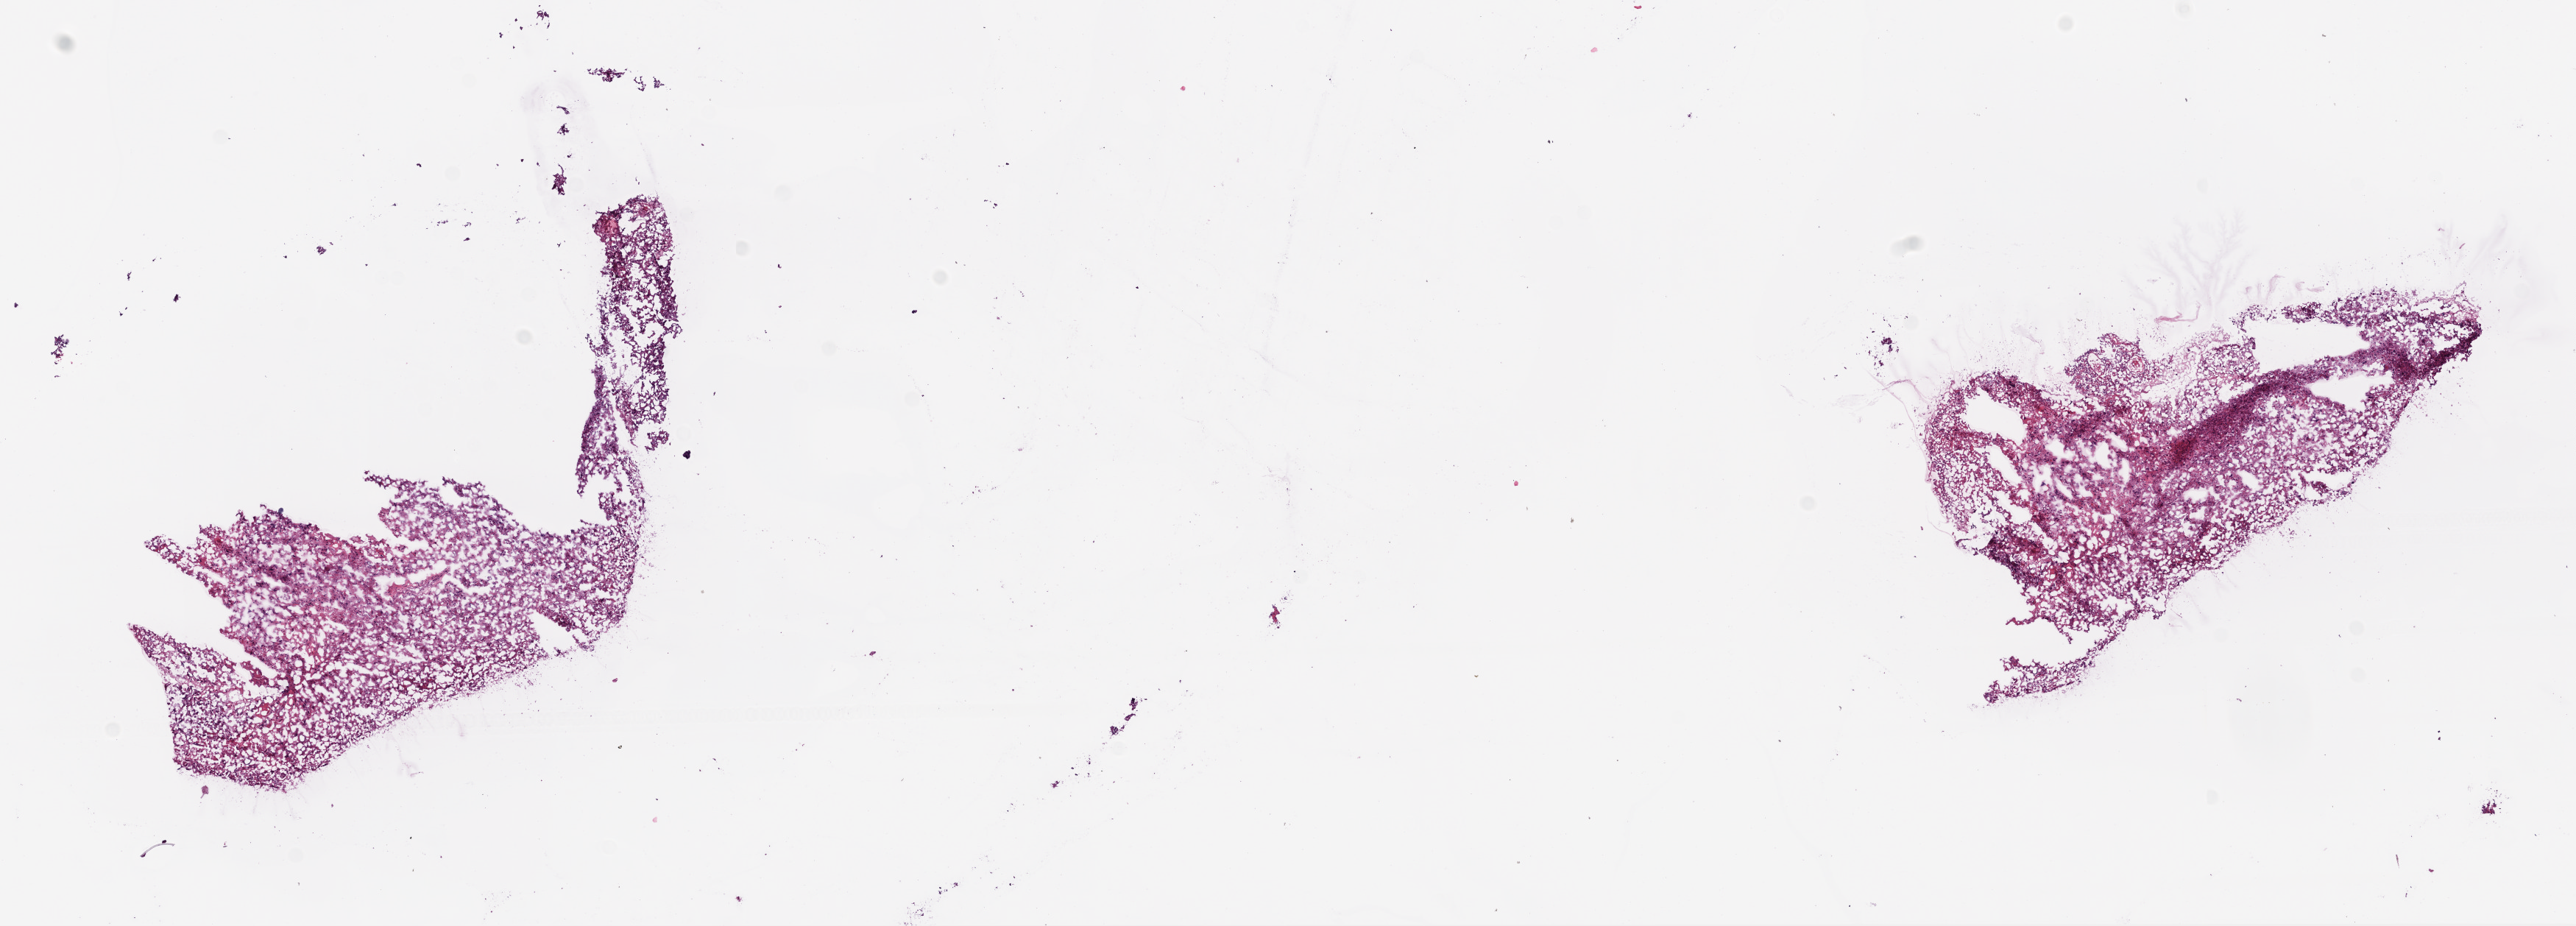
Whole-slide histology image, H&E-stained, a low-resolution overview of the entire scanned area, about 14.0 x 5.0 mm (acquisition: 20x scan); frozen section from the bottom of the tissue portion; primary tumour sample from the brain. Male, age 48 years at initial diagnosis. Composition of this section per pathologist review: tumour cells 98%, tumour nuclei 85%, normal cells 0%, stromal cells 0%, necrosis 2%.
Diagnosis: Glioblastoma.